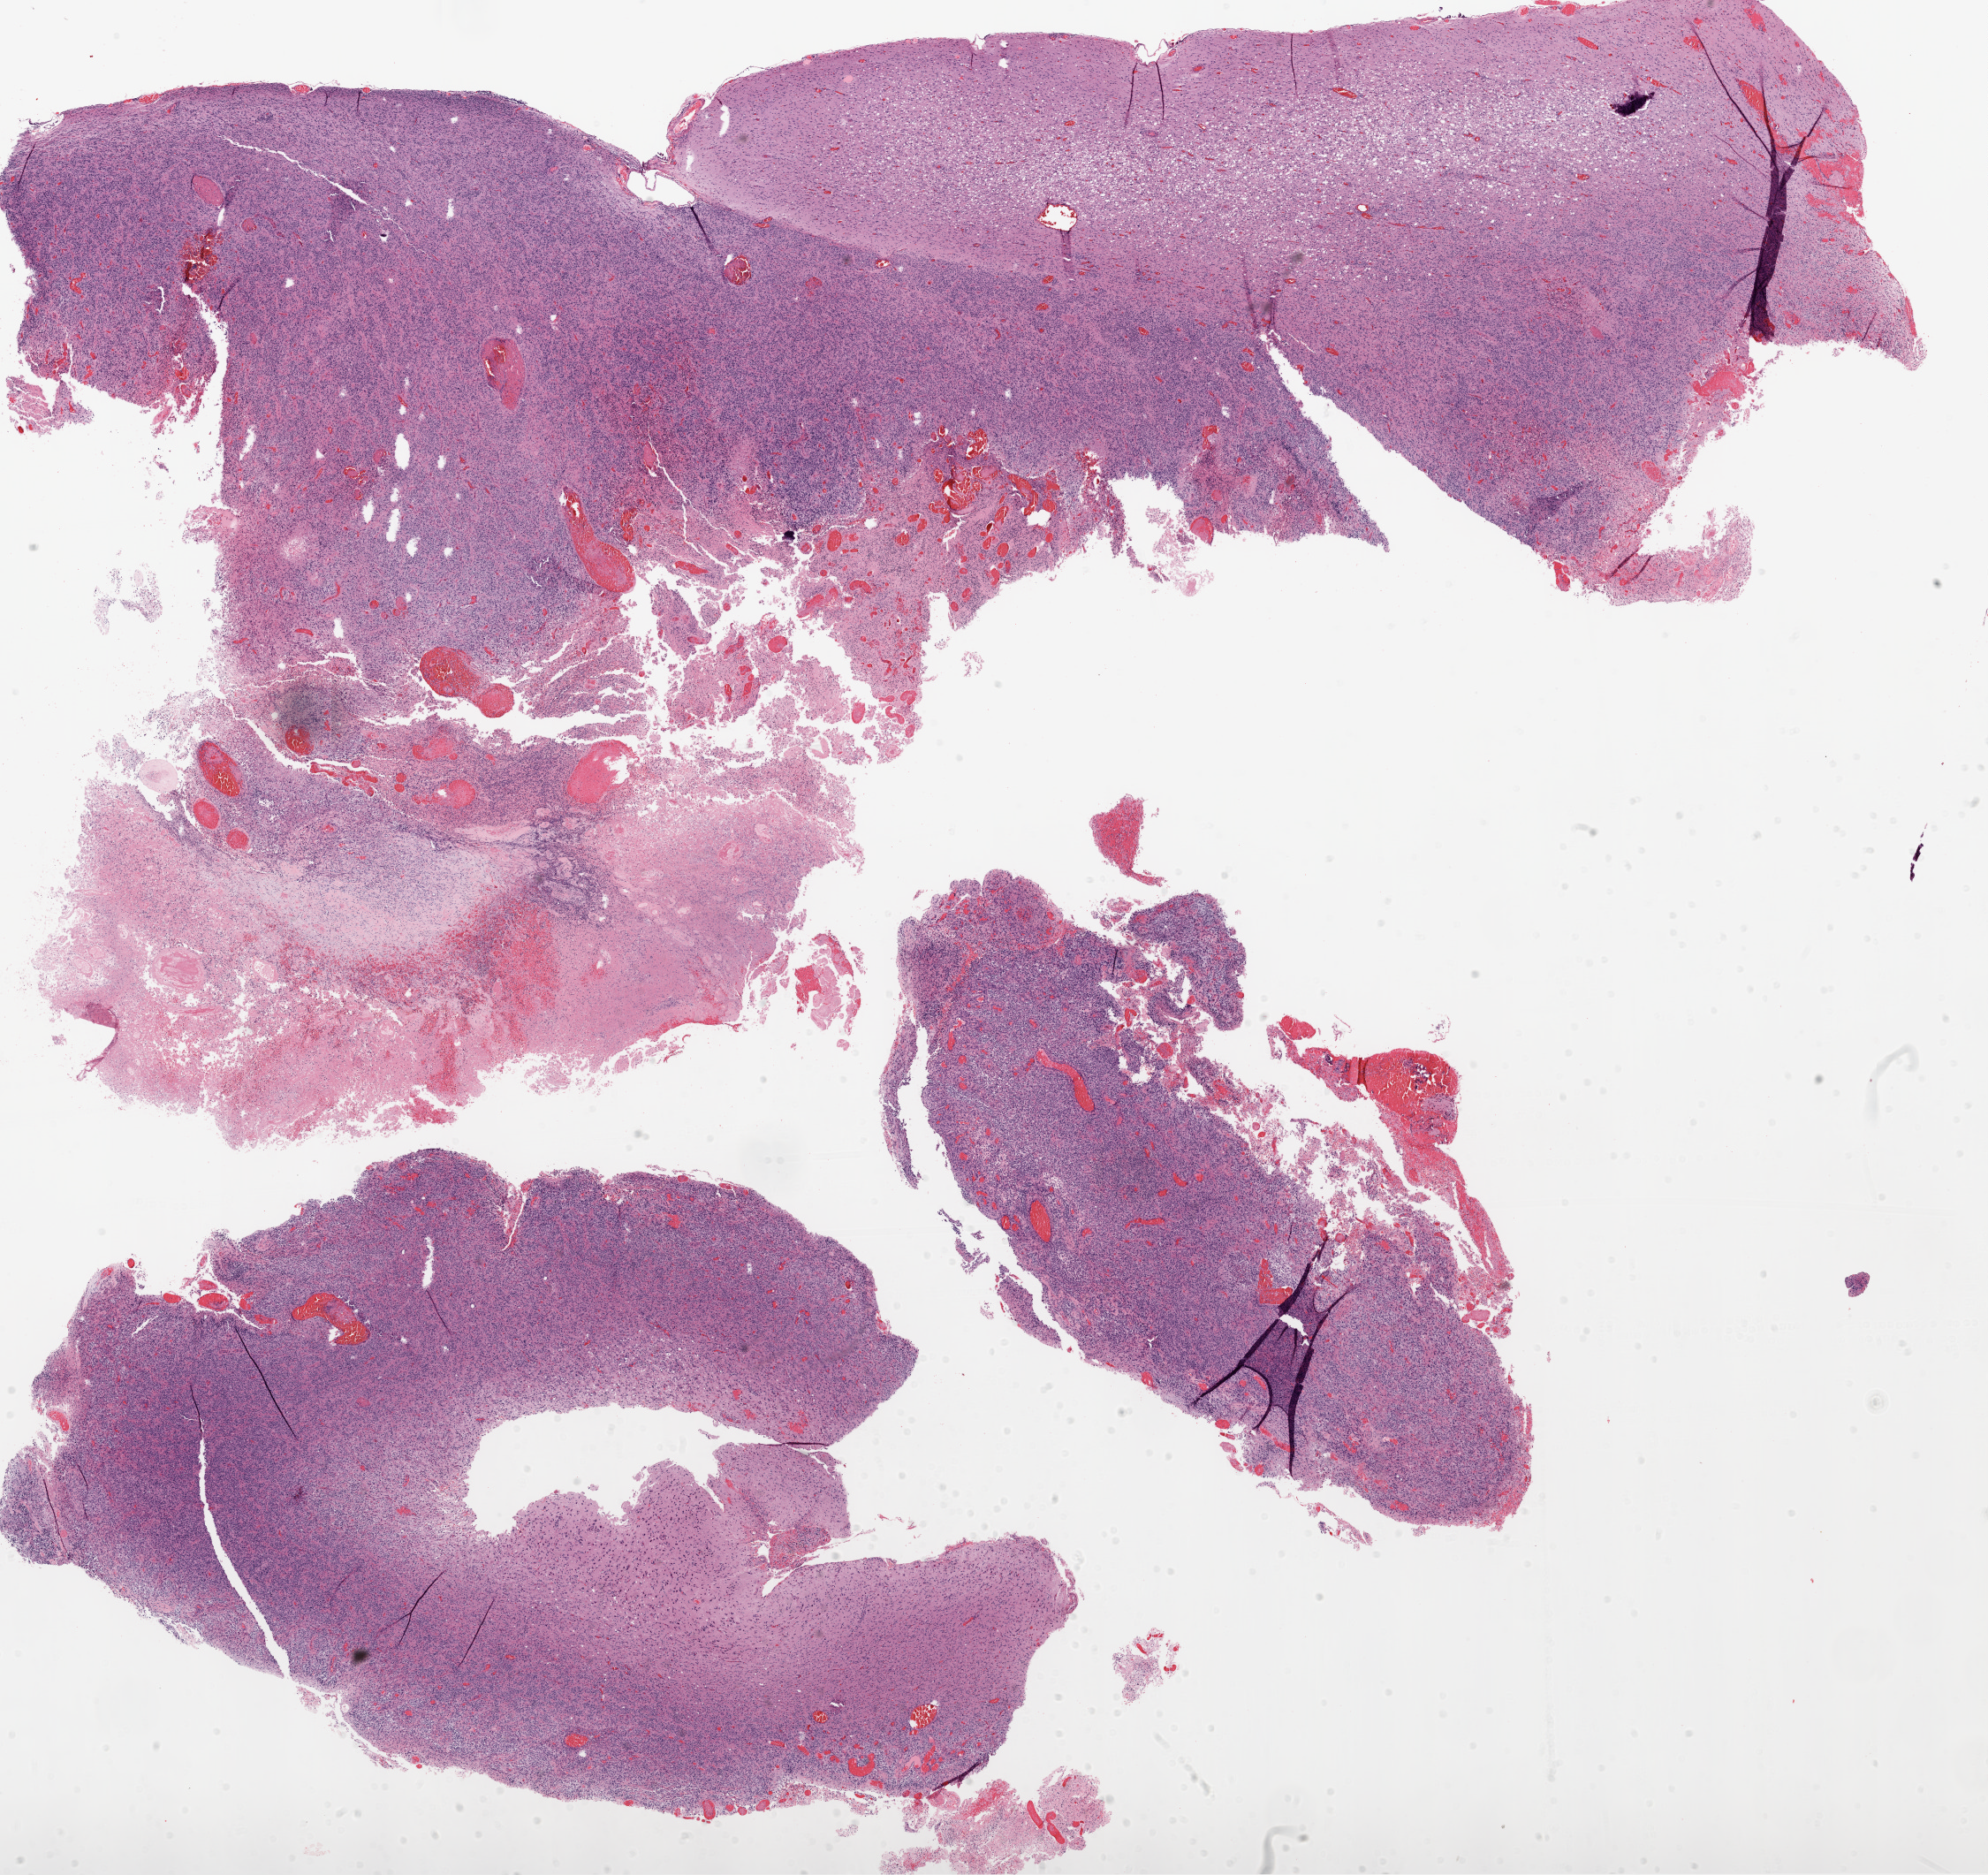
Whole-slide histology image, Hematoxylin and eosin (H&E) stained — low-resolution overview of the scanned area, about 18.1 x 17.0 mm. Formalin-fixed paraffin-embedded (FFPE) diagnostic section. Brain, primary tumour sample. Male, age 39 years at initial diagnosis.
Pathologic diagnosis: Glioblastoma.